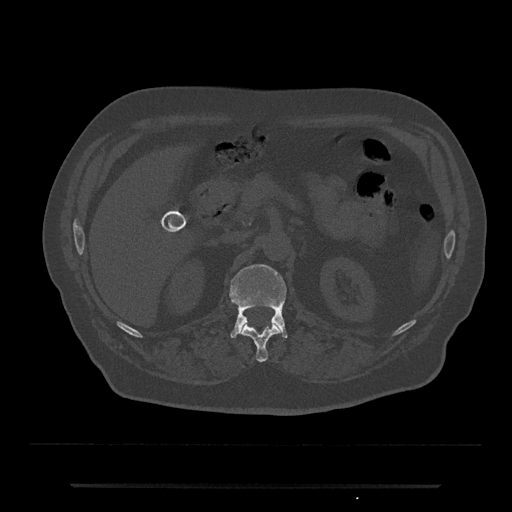
CT including the spine, one axial slice. Slice 560 of 797 in the series (ordered by position). Reconstruction kernel Br40s/3. Bone window (W 1800 / L 400 HU). 0.5 mm slice thickness. 512 × 512 image matrix, field of view 434 × 434 mm. Male patient, age 80 years. From the clinical record (not read from this slice): primary cancer: prostate.
Outlined on this slice (semi-automatic segmentation, software-assisted and operator-edited):
- L1 vertebra: box from (x=230, y=264) to (x=287, y=339) px
- T12 vertebra: (x=242, y=324)–(x=280, y=362)